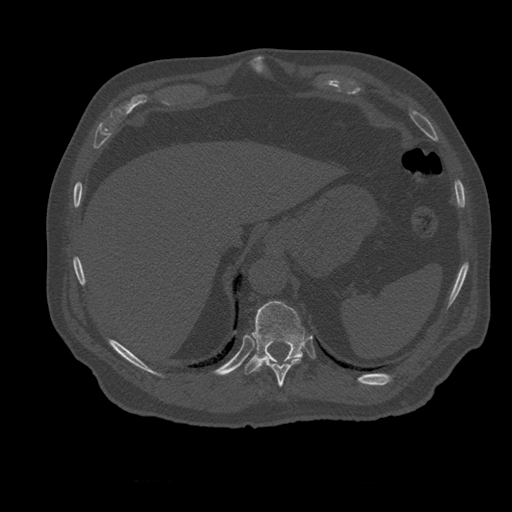
CT including the spine, one axial slice. Slice 289 of 399 in the series (ordered by position). Reconstruction kernel STANDARD. Bone window (W 1800 / L 400 HU). 1.25 mm slice thickness. 512 × 512 image matrix. Patient age 73 years. Case-level facts recorded for this patient, not image findings: primary cancer: prostate; vertebrae with lytic lesions (as recorded): L2.
Annotated regions visible in this slice (semi-automatic segmentation, software-assisted and operator-edited):
- T10 vertebra: box from (x=261, y=359) to (x=302, y=387) px
- T11 vertebra: (x=245, y=301)–(x=306, y=375)